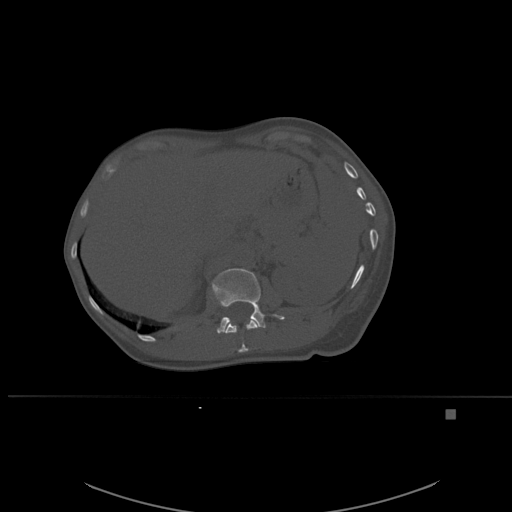
CT including the spine, one axial slice. Position 268 of 537 along the scan axis. Bone window (W 1800 / L 400 HU). 512 × 512 image matrix, field of view 440 × 440 mm. Patient: female, 45 years. Case-level facts recorded for this patient, not image findings: primary cancer: lung.
Structures marked on this image (semi-automatically segmented with operator editing):
- L1 vertebra: bounding box (x1, y1, x2, y2) in pixels: (212, 268, 285, 334)
- T12 vertebra: (225, 319, 259, 353)